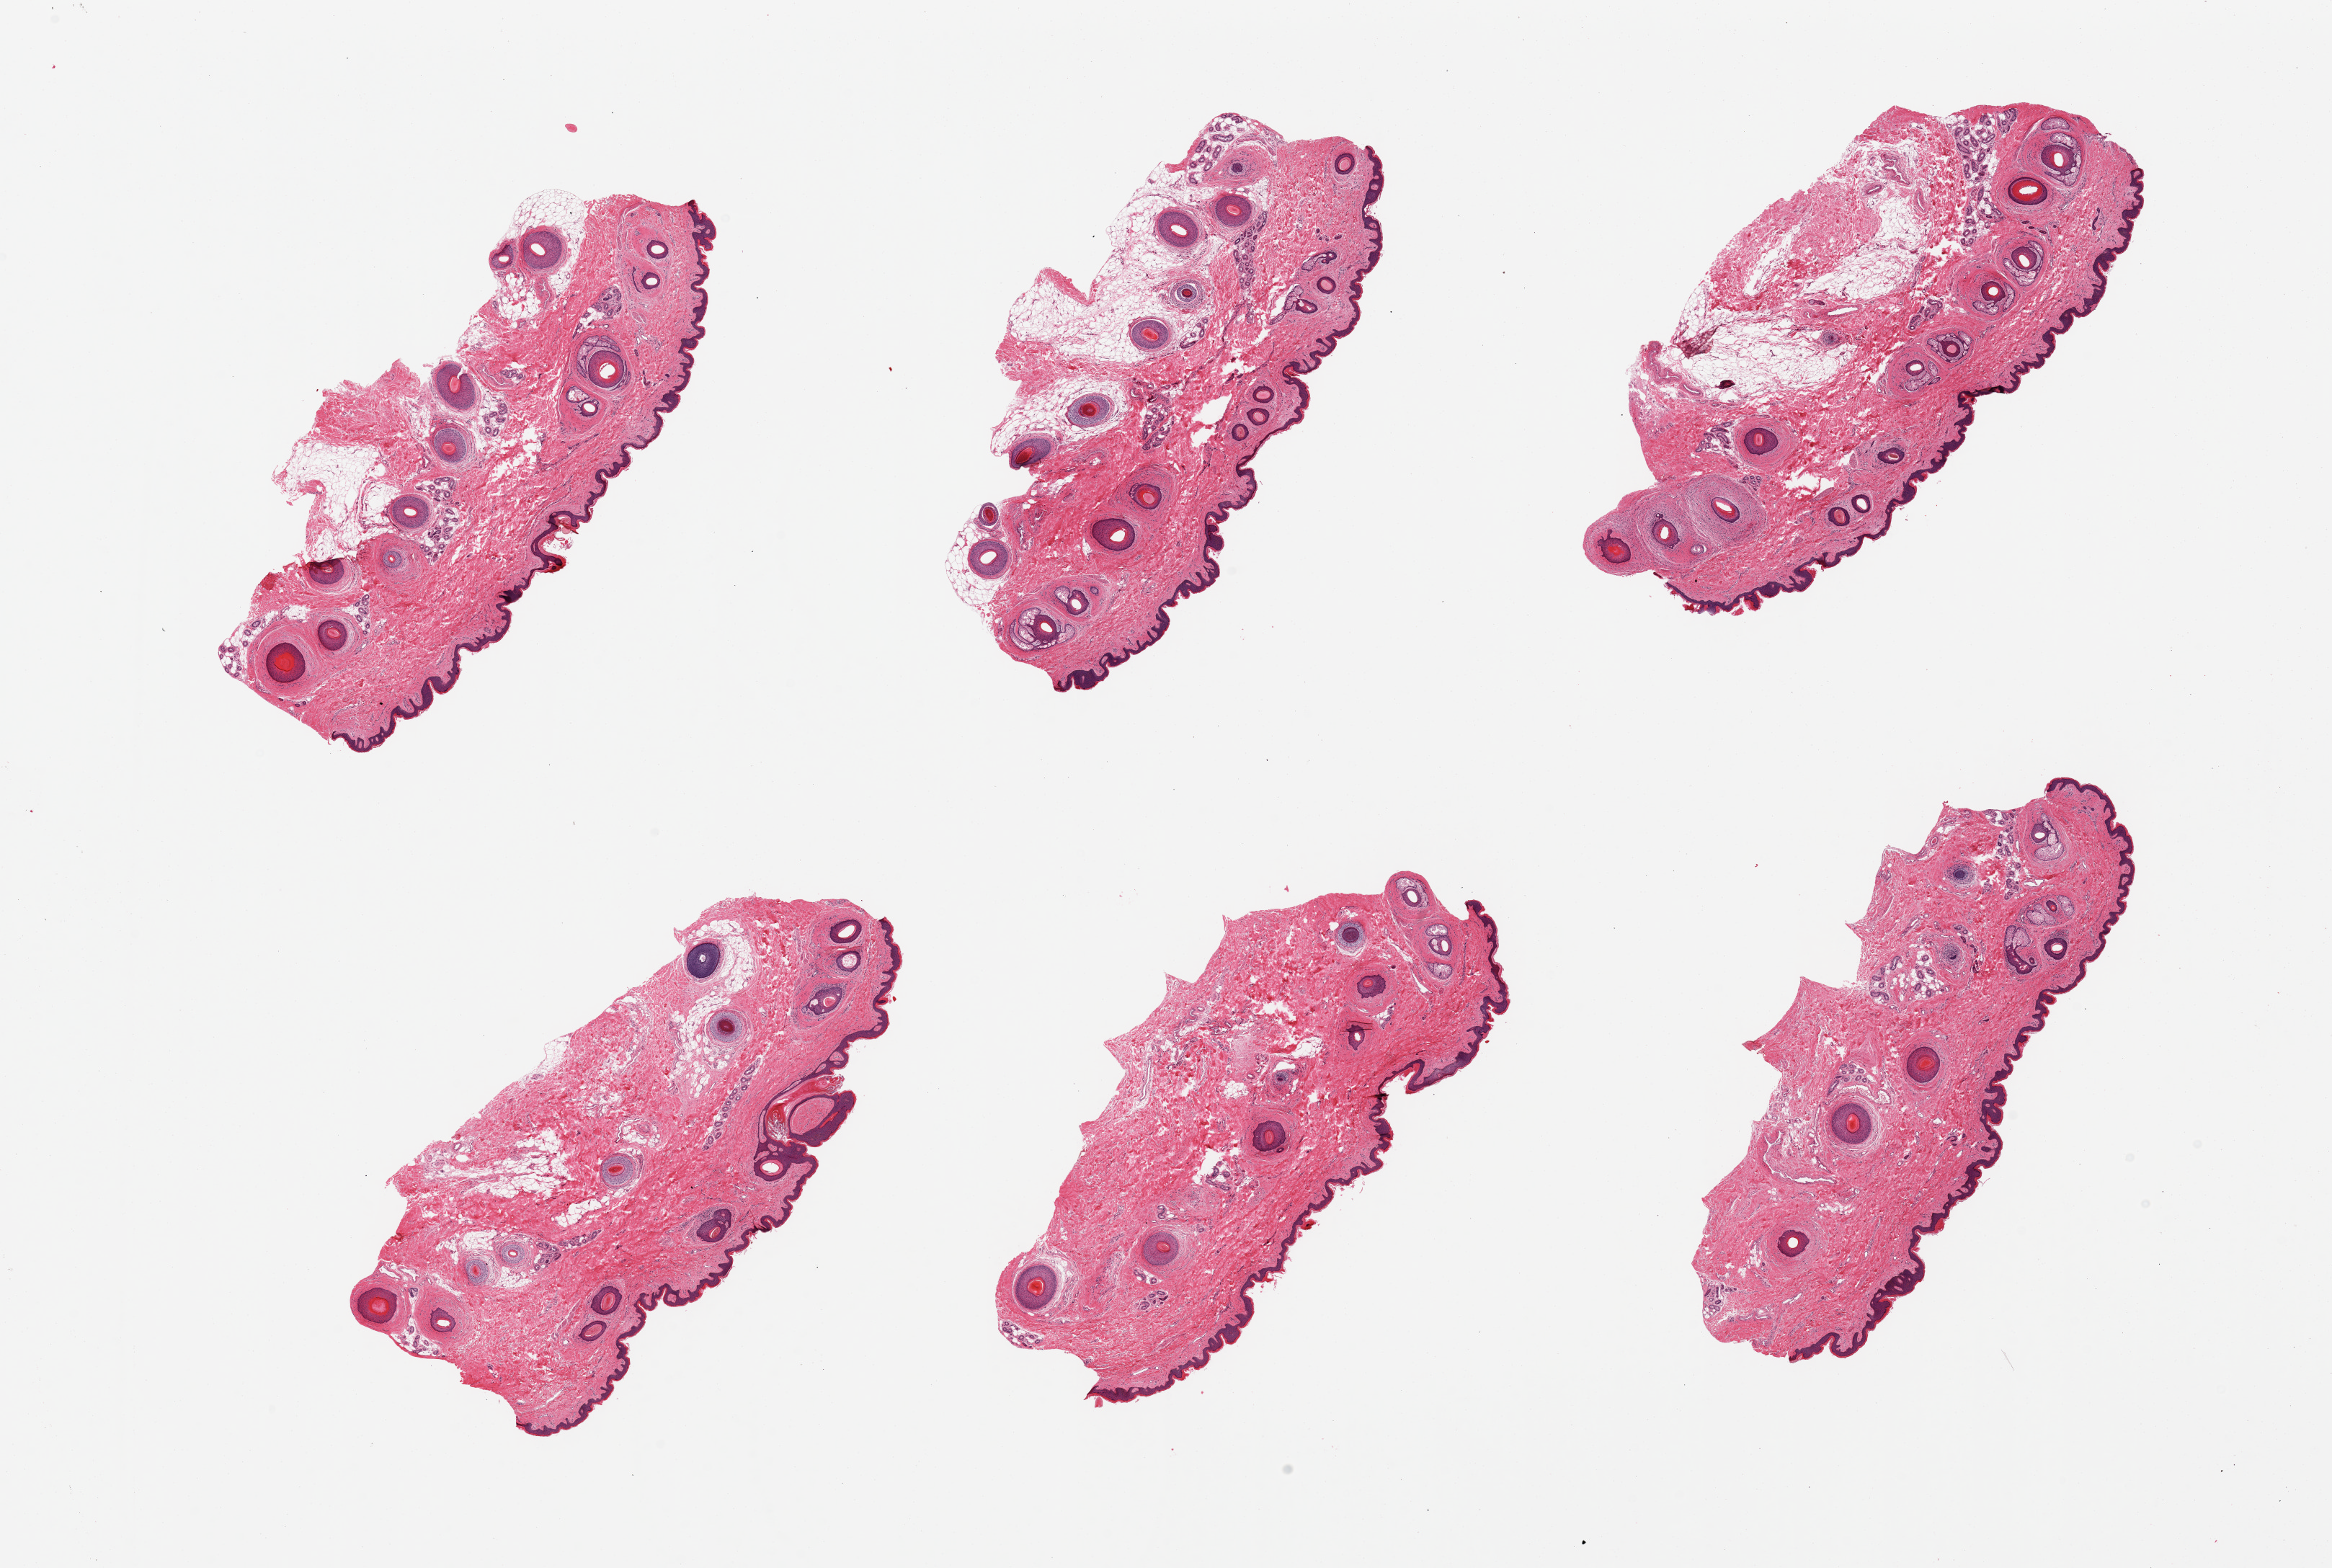
Digitized haematoxylin and eosin-stained section — shown as a low-resolution overview of the whole scanned area (about 25.6 x 17.2 mm, from a 20x scan); PAXgene-fixed, paraffin-embedded tissue; target tissue: skin of suprapubic region; donor tissue sample. Donor sex: male.
Reviewer comment on this tissue sample: 6 pieces; many hair follicles;(avoid pubic hair); well trimmed of subcutaneous fat.